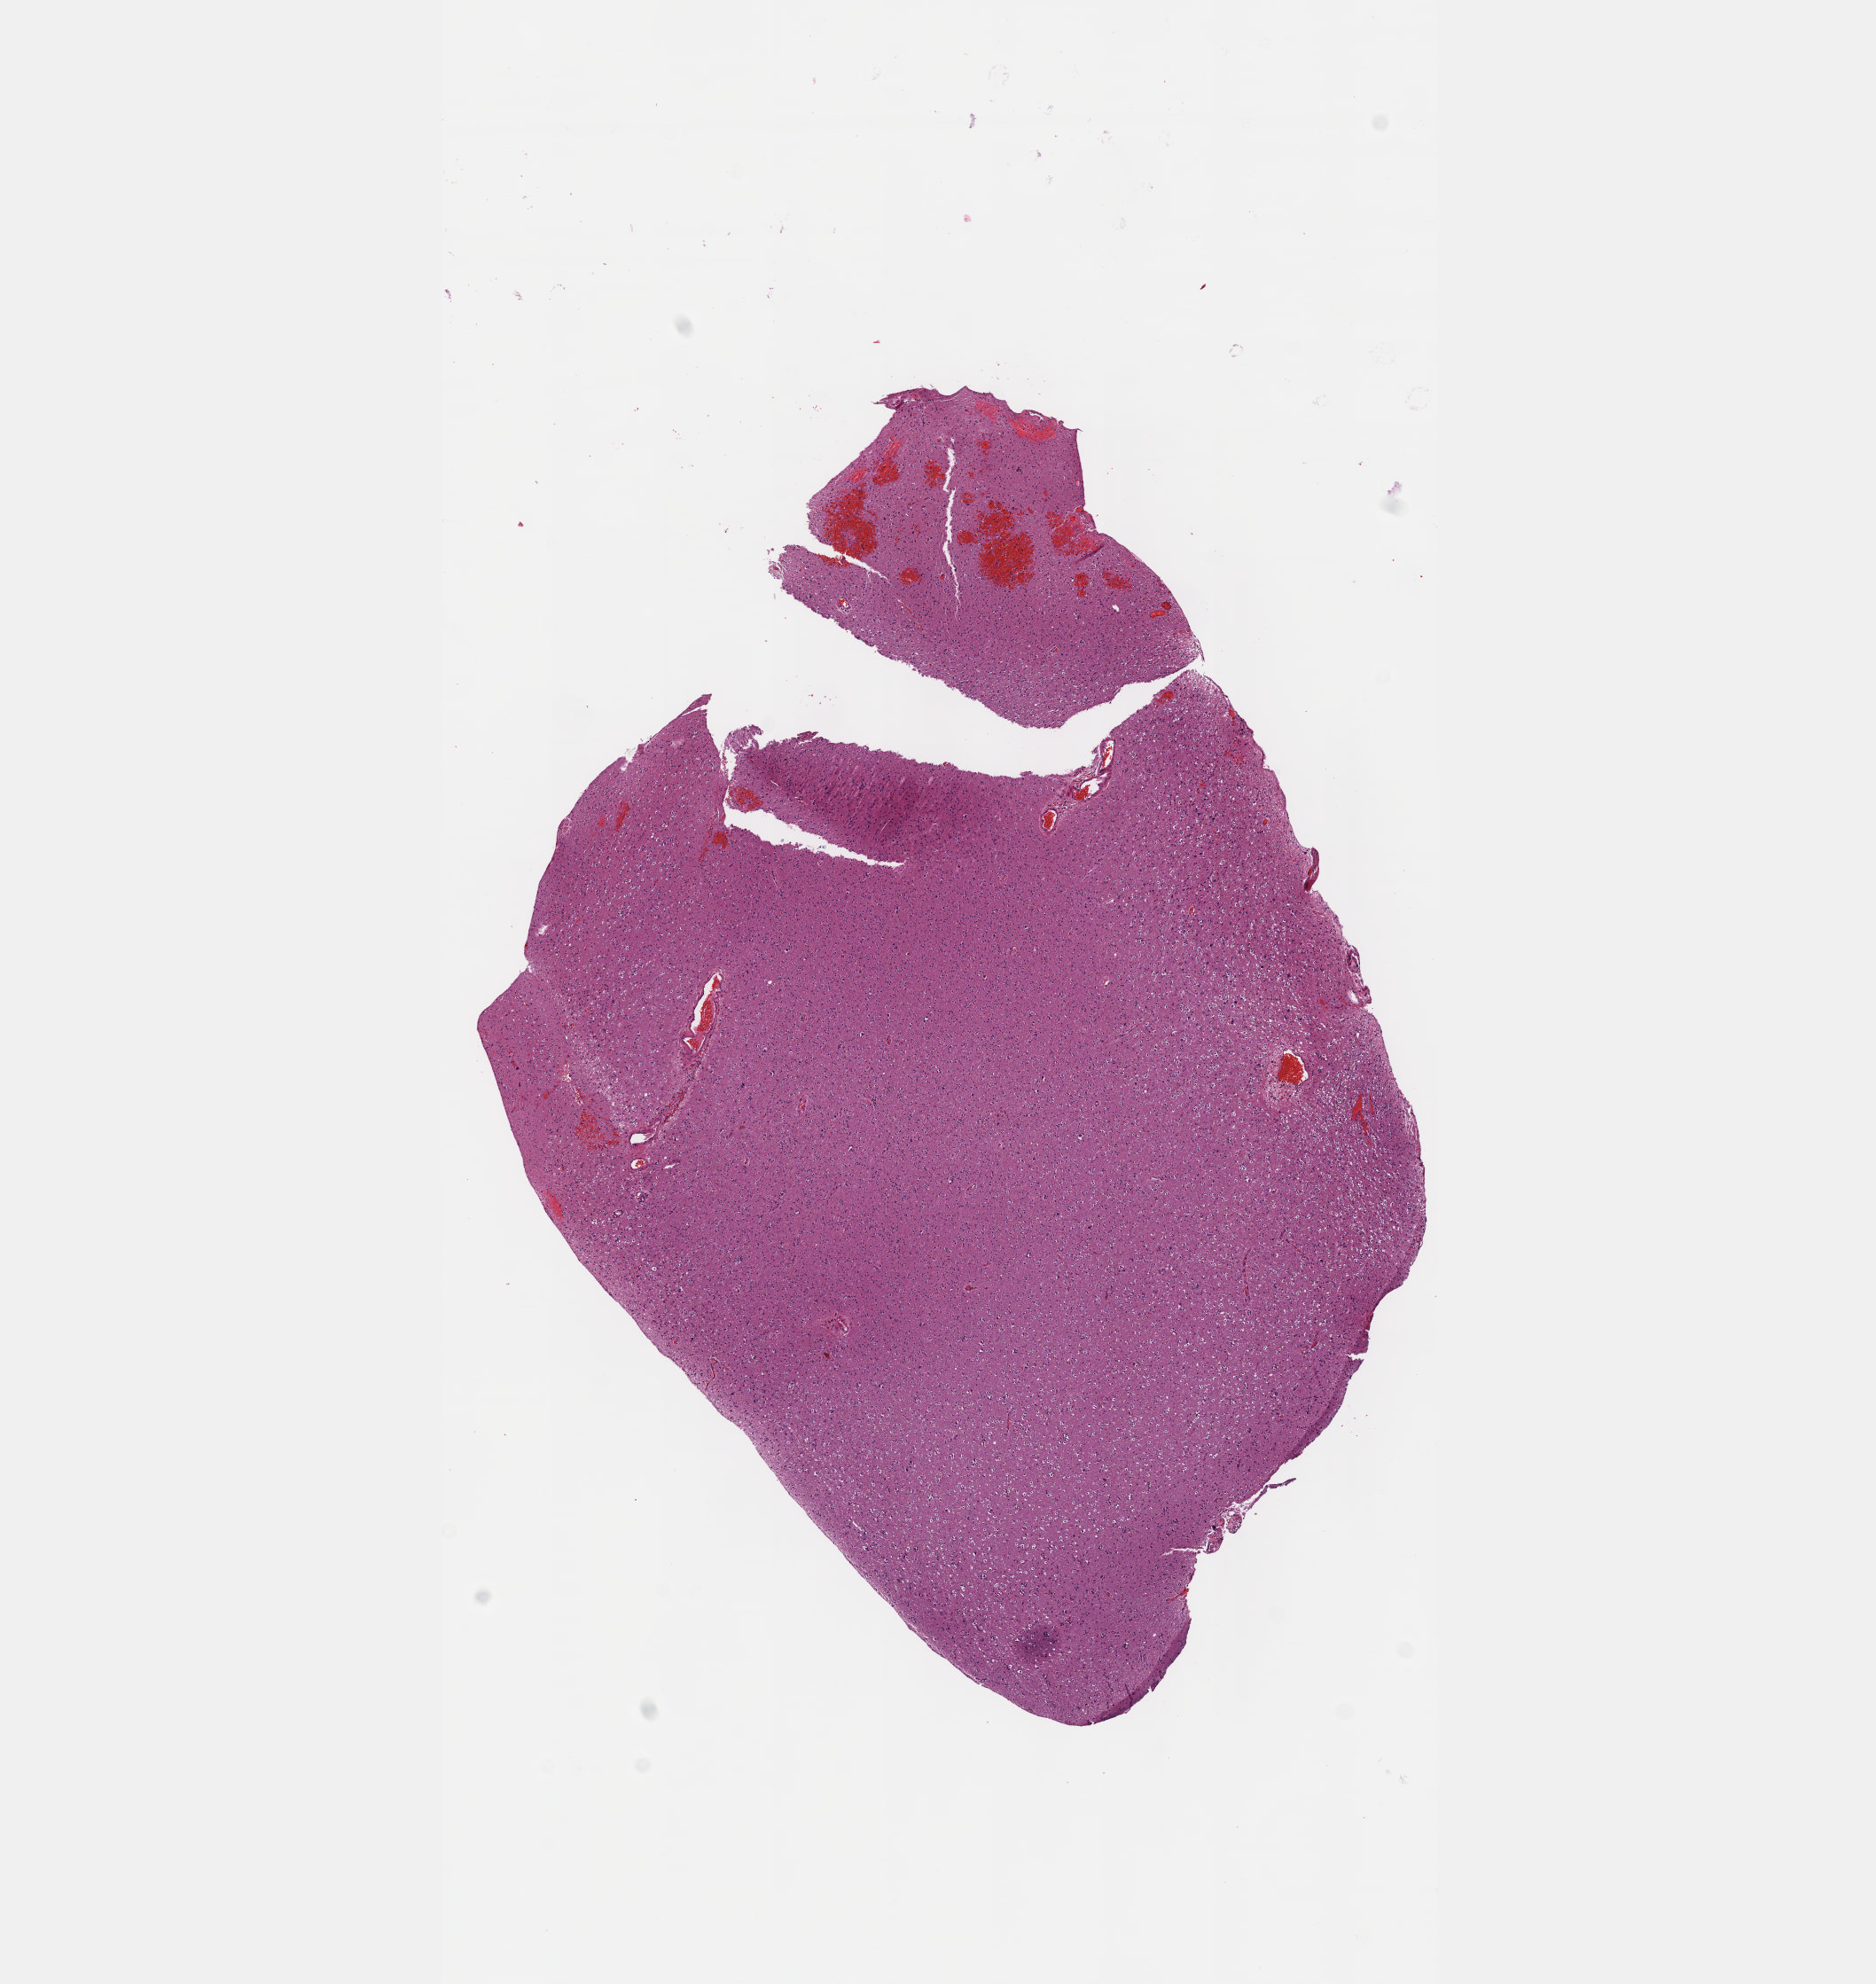
Whole-slide histology image, Hematoxylin and eosin (H&E) stained — low-resolution overview of the scanned area, about 8.6 x 9.0 mm (slide scanned at 40x); FFPE section; brain, primary tumour sample. Male patient; age at initial diagnosis 38 years. Histologic grade: G2 (moderately differentiated).
Diagnosis: Oligodendroglioma, NOS (cerebrum). Laterality: left.